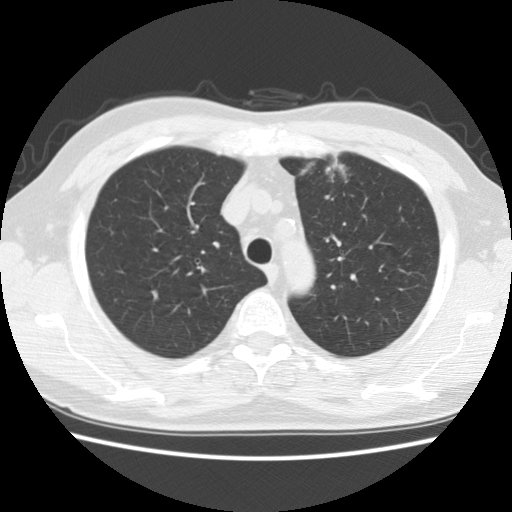
Low-dose screening chest CT, one axial slice. Slice 131 of 172 in the series (ordered by position). 120 kVp. Lung window (W 1500 / L -600 HU). 2.5 mm slice thickness. 512 × 512 image matrix, field of view 337 × 337 mm.
Annotated regions visible in this slice (outlined manually by an expert reader):
- lesion 1 (tumor, upper lobe of left lung): box from (x=325, y=161) to (x=346, y=182) px